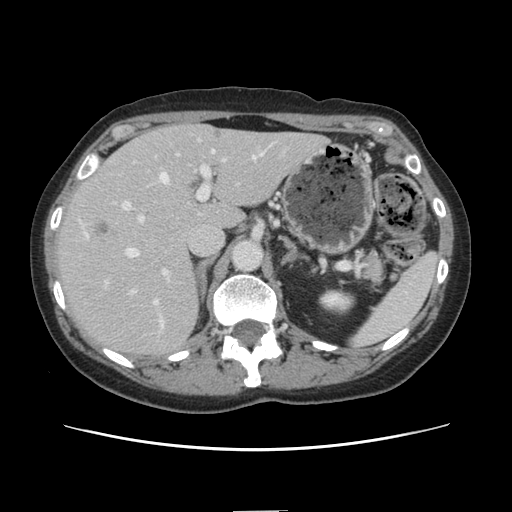
Contrast-enhanced abdominal CT, one axial slice. Position 89 of 141 along the scan axis. 120 kVp. Intravenous contrast given. Soft-tissue window (W 400 / L 40 HU). 2.5 mm slice thickness. 512 × 512 image matrix, field of view 350 × 350 mm. Female patient, age 63 years. From the clinical record (not read from this slice): diagnosis: colorectal cancer liver metastases, imaged before liver resection; multiple liver metastases: yes; largest metastasis: 3.2 cm.
Structures marked on this image (manually delineated by an expert):
- hepatic veins: bounding box (x1, y1, x2, y2) in pixels: (106, 151, 262, 329)
- liver: (57, 125, 326, 357)
- planned liver remnant (the part of the liver to remain after resection): (178, 125, 327, 229)
- portal vein (with intrahepatic branches): (120, 150, 229, 293)